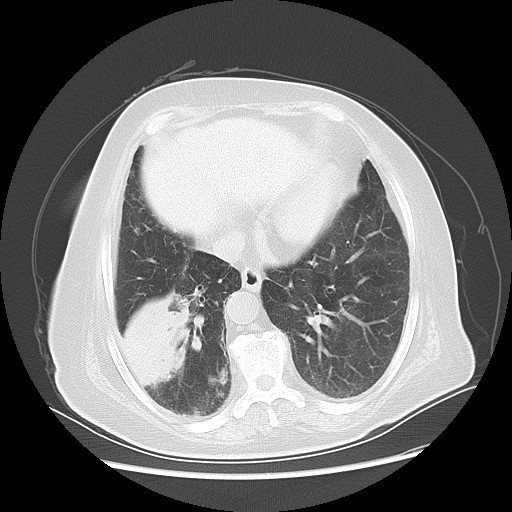
Chest CT, one axial slice; slice 19 of 56 in the series (ordered by position); reconstruction kernel LUNG; lung window (W 1500 / L -600 HU); 5 mm slice thickness; 512 × 512 image matrix. Patient: female, 73 years. From the clinical record (not read from this slice): clinical TNM (as recorded): T3 N0 M0.
Annotated regions visible in this slice (bounding box drawn by a radiologist):
- lung tumour (recorded histology: adenocarcinoma): bounding box (x1, y1, x2, y2) in pixels: (116, 283, 201, 395)